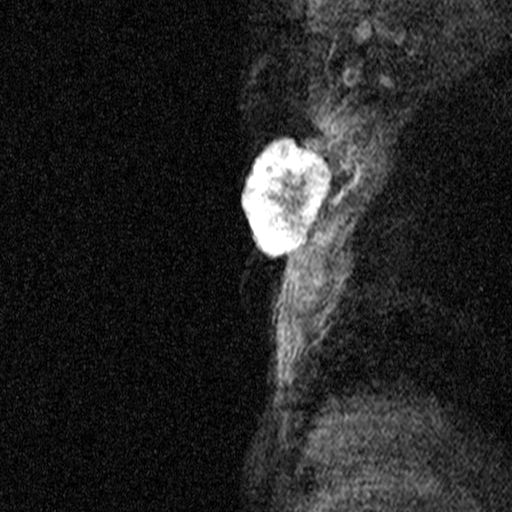
Breast MRI (dynamic contrast-enhanced), one sagittal slice. Slice 34 of 44 in the series (ordered by position). Dynamic contrast-enhanced study with each time point stored as its own series, time point 2 of 3 at this slice position (early post-contrast, ordered by acquisition time). 1.5 T. TE 4.5 ms, TR 11 ms. 3 mm slice thickness. 512 × 512 image matrix, field of view 200 × 200 mm. Patient: female, 44 years. From the clinical record (not read from this slice): setting: breast cancer imaged before/during neoadjuvant chemotherapy; receptor status: HR-positive, HER2-negative.
Structures marked on this image (semi-automatic segmentation, software-assisted and operator-edited):
- analysis volume of interest (the breast-tissue region the enhancement analysis was run in; not a lesion): bounding box <218,118,332,291> (left, top, right, bottom; pixels)
- tumour enhancement mask (voxels above the 90 % enhancement threshold inside the analysis volume of interest): <241,137,331,256>